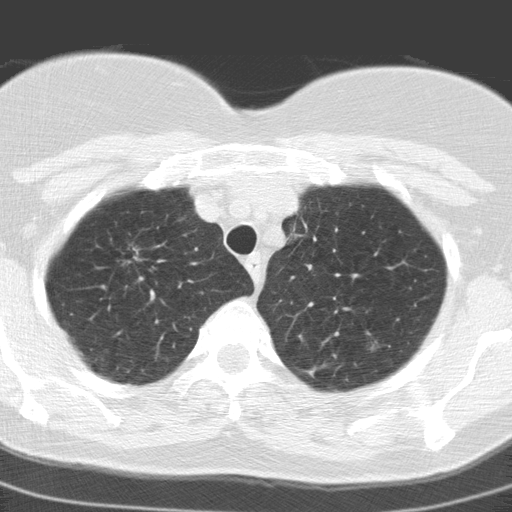
Chest CT (low-dose screening protocol), one axial image, baseline screening round, lung window (W 1500 / L -600 HU), 3.2 mm slice thickness, slice 27 of 165 in the series, 512 × 512 image matrix. Female participant, aged 60 years at enrolment.
- Expert-annotated lung lesion, box from (x=98, y=236) to (x=162, y=285) px.
- Screening reader's record for this exam: no non-calcified nodule ≥4 mm recorded.
- Participant outcome: lung cancer diagnosed 447 days after this screen — adenocarcinoma, NOS, right upper lobe, moderately differentiated (G2), stage IA (AJCC 6th edition), 23 mm at pathology.